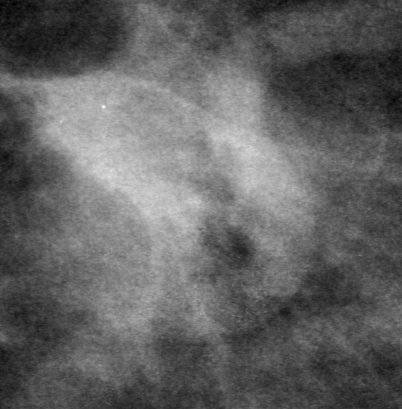
Region of interest cut from a scanned film mammogram (one marked finding), left breast, MLO view, BI-RADS breast density category 2 (scale 1–4).
Mass, shape irregular, margins ill defined; BI-RADS assessment category 0; subtlety rating 4 on a 1 (subtle) to 5 (obvious) scale; pathology (as recorded): malignant.